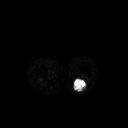
FDG PET of an extremity soft-tissue mass (from a PET/CT study), one axial slice. Slice 194 of 267 in the series (ordered by position). 3.27 mm slice thickness. 128 × 128 image matrix. Patient: male, 54 years. From the clinical record (not read from this slice): histological type: synovial sarcoma; site of the primary tumour: left poplietal fossa.
Outlined on this slice (expert contour drawn on MRI and transferred to this co-registered scan by the dataset authors):
- gross tumour volume (mass): bounding box <72,79,89,93> (left, top, right, bottom; pixels)